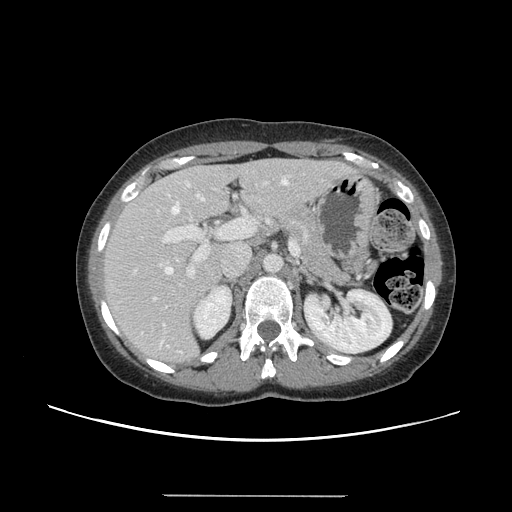
Contrast-enhanced abdominal CT, one axial slice. Slice 84 of 144 in the series (ordered by position). Intravenous contrast given. Soft-tissue window (W 400 / L 40 HU). 2.5 mm slice thickness. 512 × 512 image matrix, field of view 380 × 380 mm. Female patient, age 53 years. From the clinical record (not read from this slice): diagnosis: colorectal cancer liver metastases, imaged before liver resection; multiple liver metastases: yes.
Annotated regions visible in this slice (expert manual segmentation):
- hepatic veins: box from (x=163, y=180) to (x=288, y=326) px
- liver: (x=106, y=160)–(x=350, y=363)
- planned liver remnant (the part of the liver to remain after resection): (x=106, y=160)–(x=315, y=297)
- portal vein (with intrahepatic branches): (x=134, y=182)–(x=300, y=301)